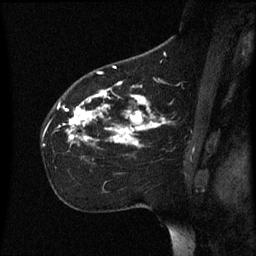
Breast MRI (dynamic contrast-enhanced), one sagittal slice. Position 39 of 60 along the scan axis. Dynamic contrast-enhanced series, image 2 of 3 at this slice position (ordered by acquisition). 1.5 T. TE 4.2 ms, TR 8.4 ms. 2.2 mm slice thickness. 256 × 256 image matrix. Patient: female, 35 years. Case-level facts recorded for this patient, not image findings: setting: breast cancer imaged before/during neoadjuvant chemotherapy; receptor status: HER2-positive.
Annotated regions visible in this slice (semi-automatic segmentation, software-assisted and operator-edited):
- analysis volume of interest (the breast-tissue region the enhancement analysis was run in; not a lesion): bounding box (x1, y1, x2, y2) in pixels: (43, 78, 173, 161)
- tumour enhancement mask (voxels above the 70 % enhancement threshold inside the analysis volume of interest): (63, 82, 170, 147)